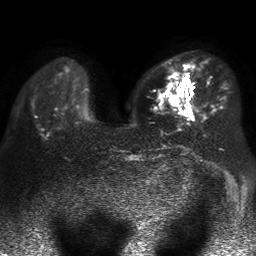
Breast MRI, one axial slice; position 17 of 50 along the scan axis; diffusion-weighted series; image 2 of 4 stored at this slice position (different b-values; order by instance number); 1.5 T; 4 mm slice thickness; 256 × 256 image matrix, field of view 360 × 360 mm. Female patient.
Structures marked on this image (expert manual segmentation):
- tumour on diffusion-weighted imaging: bounding box [x1, y1, x2, y2] px = [170, 97, 178, 105]